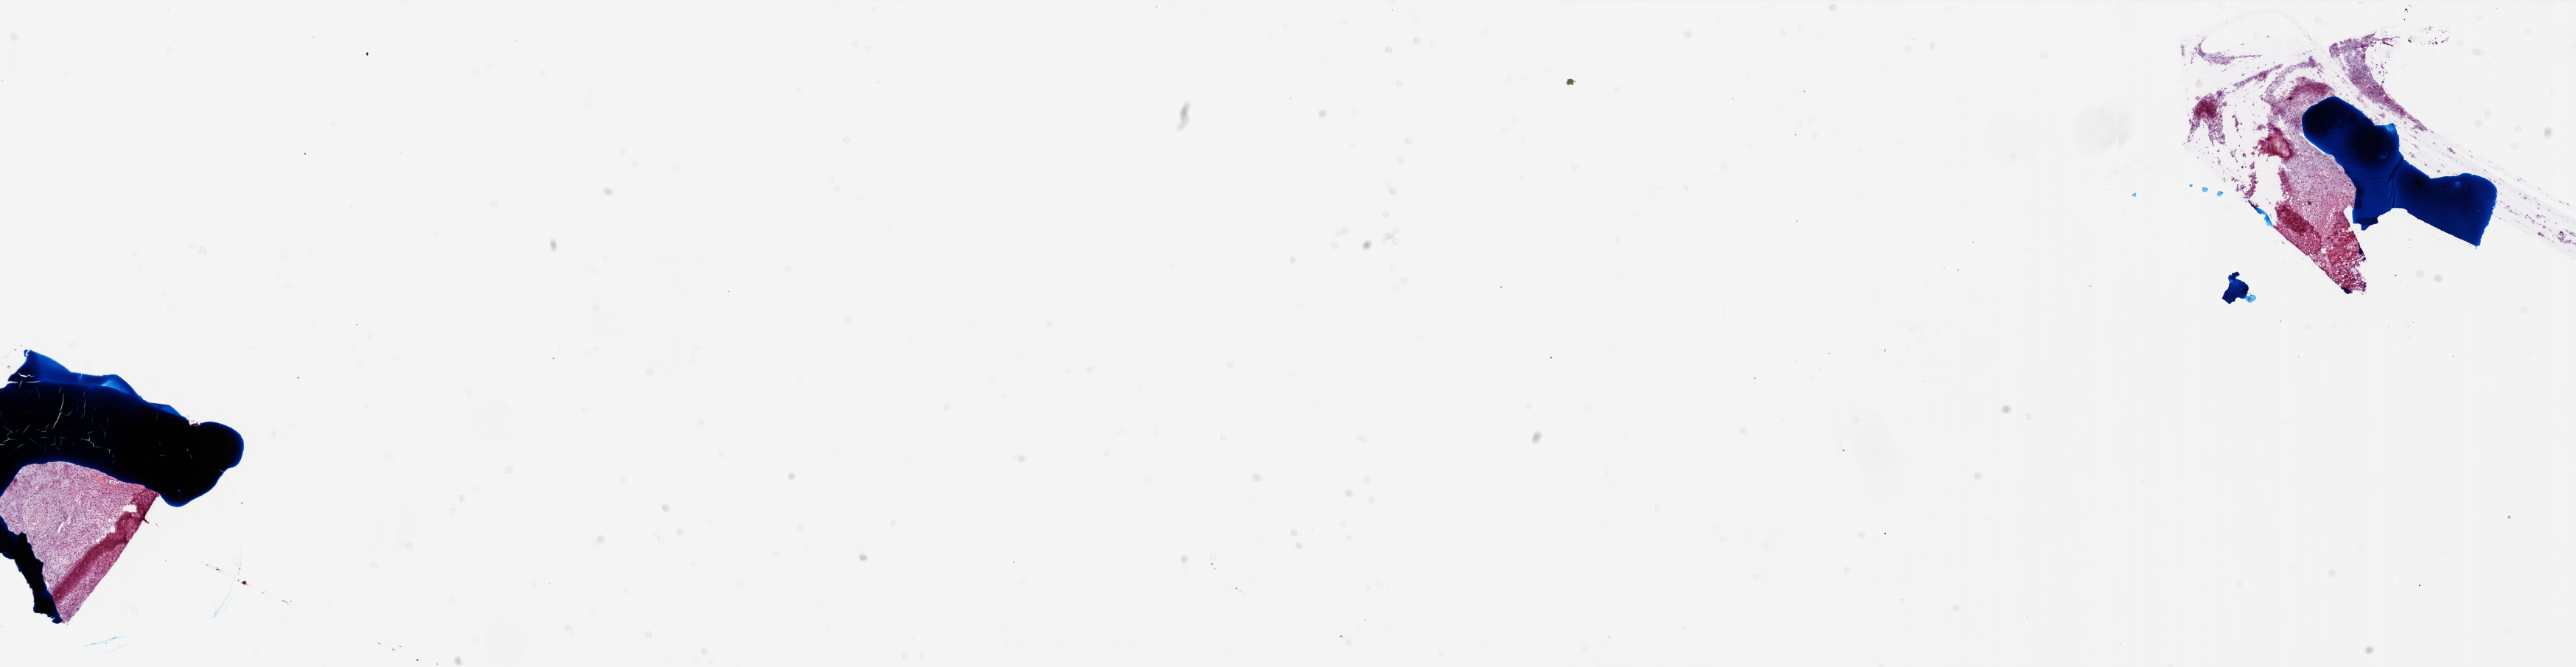
Digitized Hematoxylin and eosin (H&E) stained tissue section (whole slide), whole scanned area (about 28.0 x 7.2 mm, acquisition: 20x scan) shown as a low-resolution overview; frozen section from the top of the tissue portion; brain, primary tumour sample. Patient: male, age at initial diagnosis 40 years. Composition of this section per pathologist review: tumour cells 88%, tumour nuclei 98%, normal cells 0%, stromal cells 2%, necrosis 10%.
• pathologic diagnosis: Glioblastoma